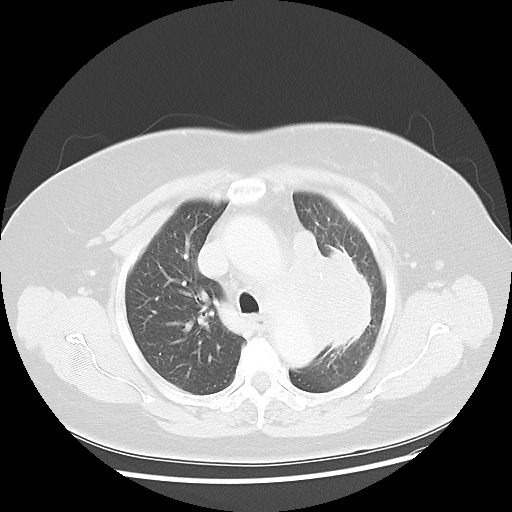
Chest CT, one axial slice. Slice 34 of 49 in the series (ordered by position). Reconstruction kernel LUNG. Lung window (W 1500 / L -600 HU). 5 mm slice thickness. 512 × 512 image matrix, field of view 374 × 374 mm. Patient: female, 58 years. Case-level facts recorded for this patient, not image findings: clinical TNM (as recorded): T4 N3 M0; histopathological grade: G3.
Outlined on this slice (rectangle marked by the reading radiologist):
- lung tumour (recorded histology: small cell carcinoma): bounding box (x1, y1, x2, y2) in pixels: (273, 212, 393, 362)